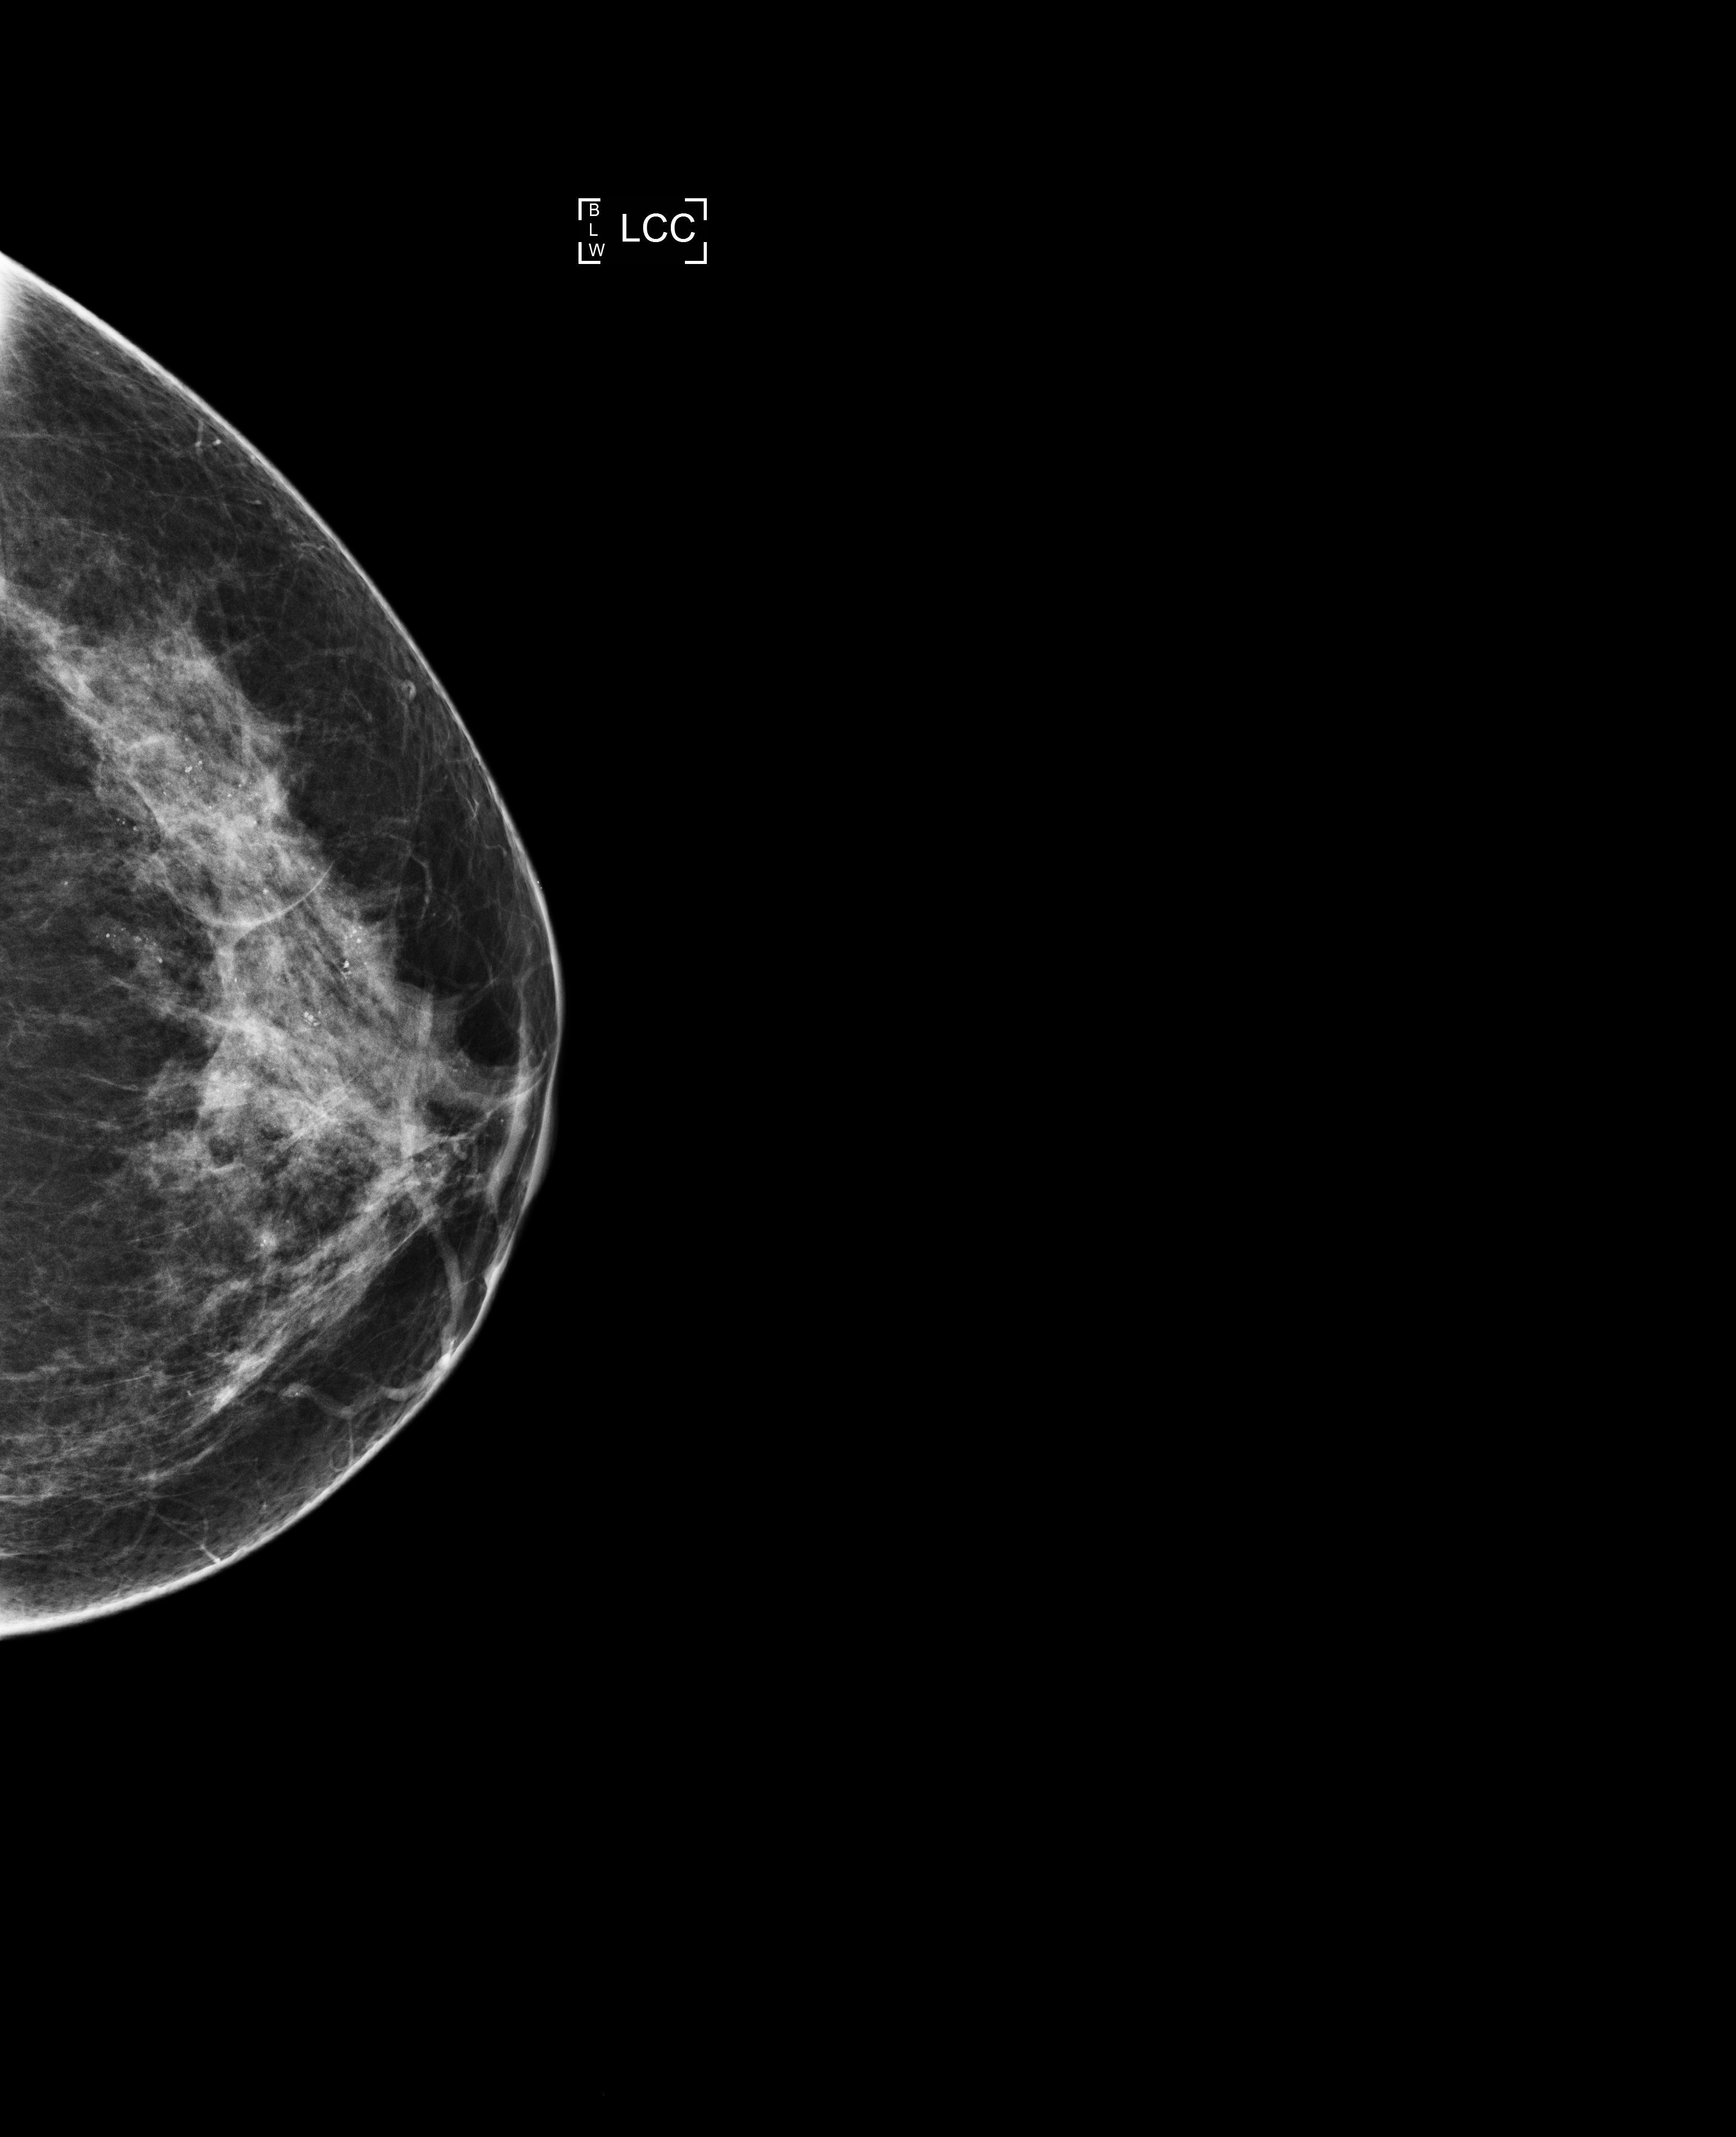
Digital mammogram (FFDM), left breast, CC view, screening examination, compressed breast thickness 59 mm. Patient aged 50 years (female).
Breast density at the screening exam (both breasts): heterogeneously dense (BI-RADS density category c). Final BI-RADS category for the screening round (tomosynthesis exam, both breasts): category 2. Recall: no recall after this screen.